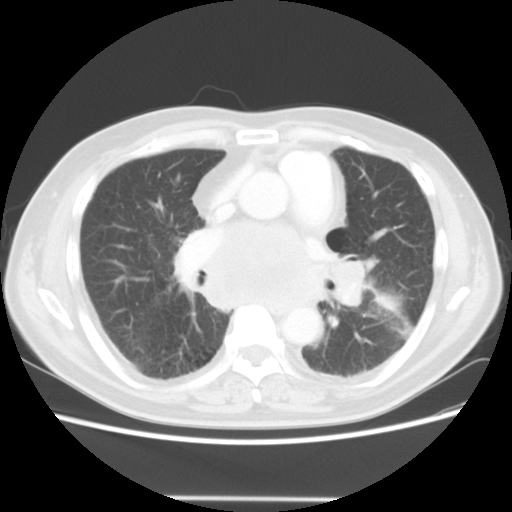
Chest CT, one axial slice. Slice 26 of 56 in the series (ordered by position). Reconstruction kernel STANDARD. 140 kVp. Lung window (W 1500 / L -600 HU). 512 × 512 image matrix, field of view 360 × 360 mm. Male patient, age 66 years. Case-level facts recorded for this patient, not image findings: clinical TNM (as recorded): T4 N3 M0.
Structures marked on this image (bounding box drawn by a radiologist):
- lung tumour (recorded histology: small cell carcinoma): bounding box <367,280,397,316> (left, top, right, bottom; pixels)